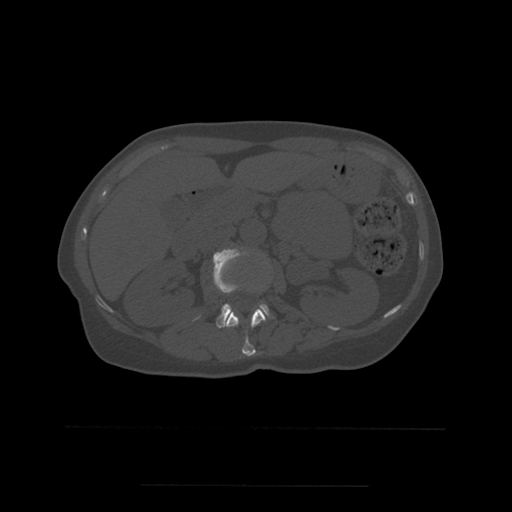
CT including the spine, one axial slice. Slice 224 of 544 in the series (ordered by position). Bone window (W 1800 / L 400 HU). 1.25 mm slice thickness. 512 × 512 image matrix, field of view 350 × 350 mm. Patient age 58 years. From the clinical record (not read from this slice): primary cancer: lung.
Structures marked on this image (semi-automatic segmentation, software-assisted and operator-edited):
- L1 vertebra: bounding box <226,309,266,357> (left, top, right, bottom; pixels)
- L2 vertebra: <196,249,270,328>